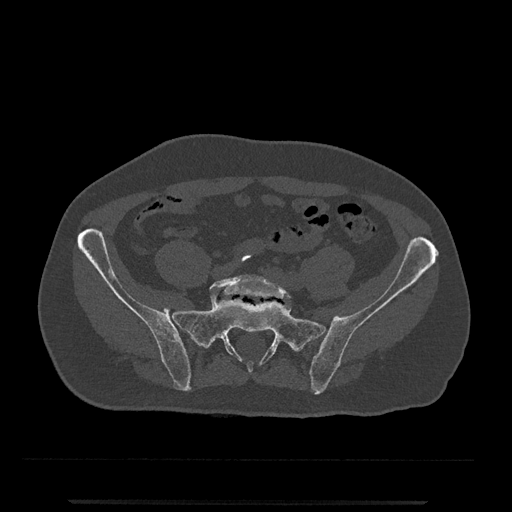
CT including the spine, one axial slice; slice 25 of 797 in the series (ordered by position); reconstruction kernel Br40s/3; 120 kVp; bone window (W 1800 / L 400 HU); 0.5 mm slice thickness; 512 × 512 image matrix. Male patient, age 63 years. Case-level facts recorded for this patient, not image findings: primary cancer: prostate.
Outlined on this slice (semi-automatic segmentation, software-assisted and operator-edited):
- L5 vertebra: bounding box <210,275,292,301> (left, top, right, bottom; pixels)